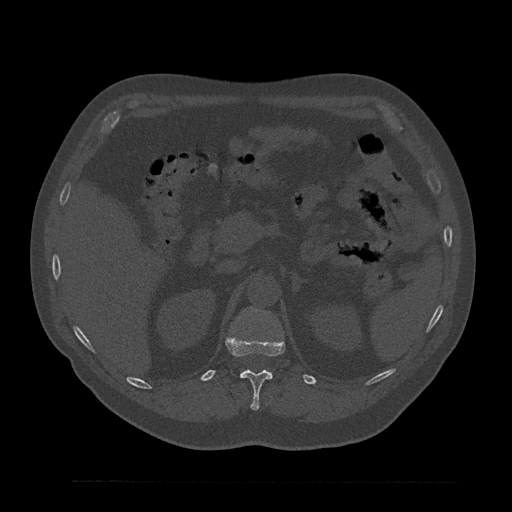
CT including the spine, one axial slice; slice 214 of 797 in the series (ordered by position); reconstruction kernel Br40s/3; 120 kVp; bone window (W 1800 / L 400 HU); 0.5 mm slice thickness; 512 × 512 image matrix, field of view 430 × 430 mm. Patient: male, 61 years. From the clinical record (not read from this slice): primary cancer: prostate.
Structures marked on this image (semi-automatic segmentation, software-assisted and operator-edited):
- T12 vertebra: bounding box <225,335,285,410> (left, top, right, bottom; pixels)